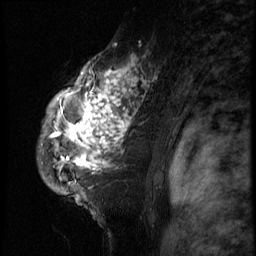
Breast MRI (dynamic contrast-enhanced), one sagittal slice; position 51 of 66 along the scan axis; 3 images stored at this slice position (order not interpretable as contrast timing); 1.5 T; TE 4.2 ms, TR 8.9 ms; 256 × 256 image matrix. Patient: female, 39 years. Case-level facts recorded for this patient, not image findings: setting: breast cancer imaged before/during neoadjuvant chemotherapy; receptor status: HER2-positive.
Annotated regions visible in this slice (semi-automatic segmentation, software-assisted and operator-edited):
- analysis volume of interest (the breast-tissue region the enhancement analysis was run in; not a lesion): box from (x=36, y=44) to (x=166, y=196) px
- tumour enhancement mask (voxels above the 140 % enhancement threshold inside the analysis volume of interest): (x=50, y=56)–(x=156, y=171)